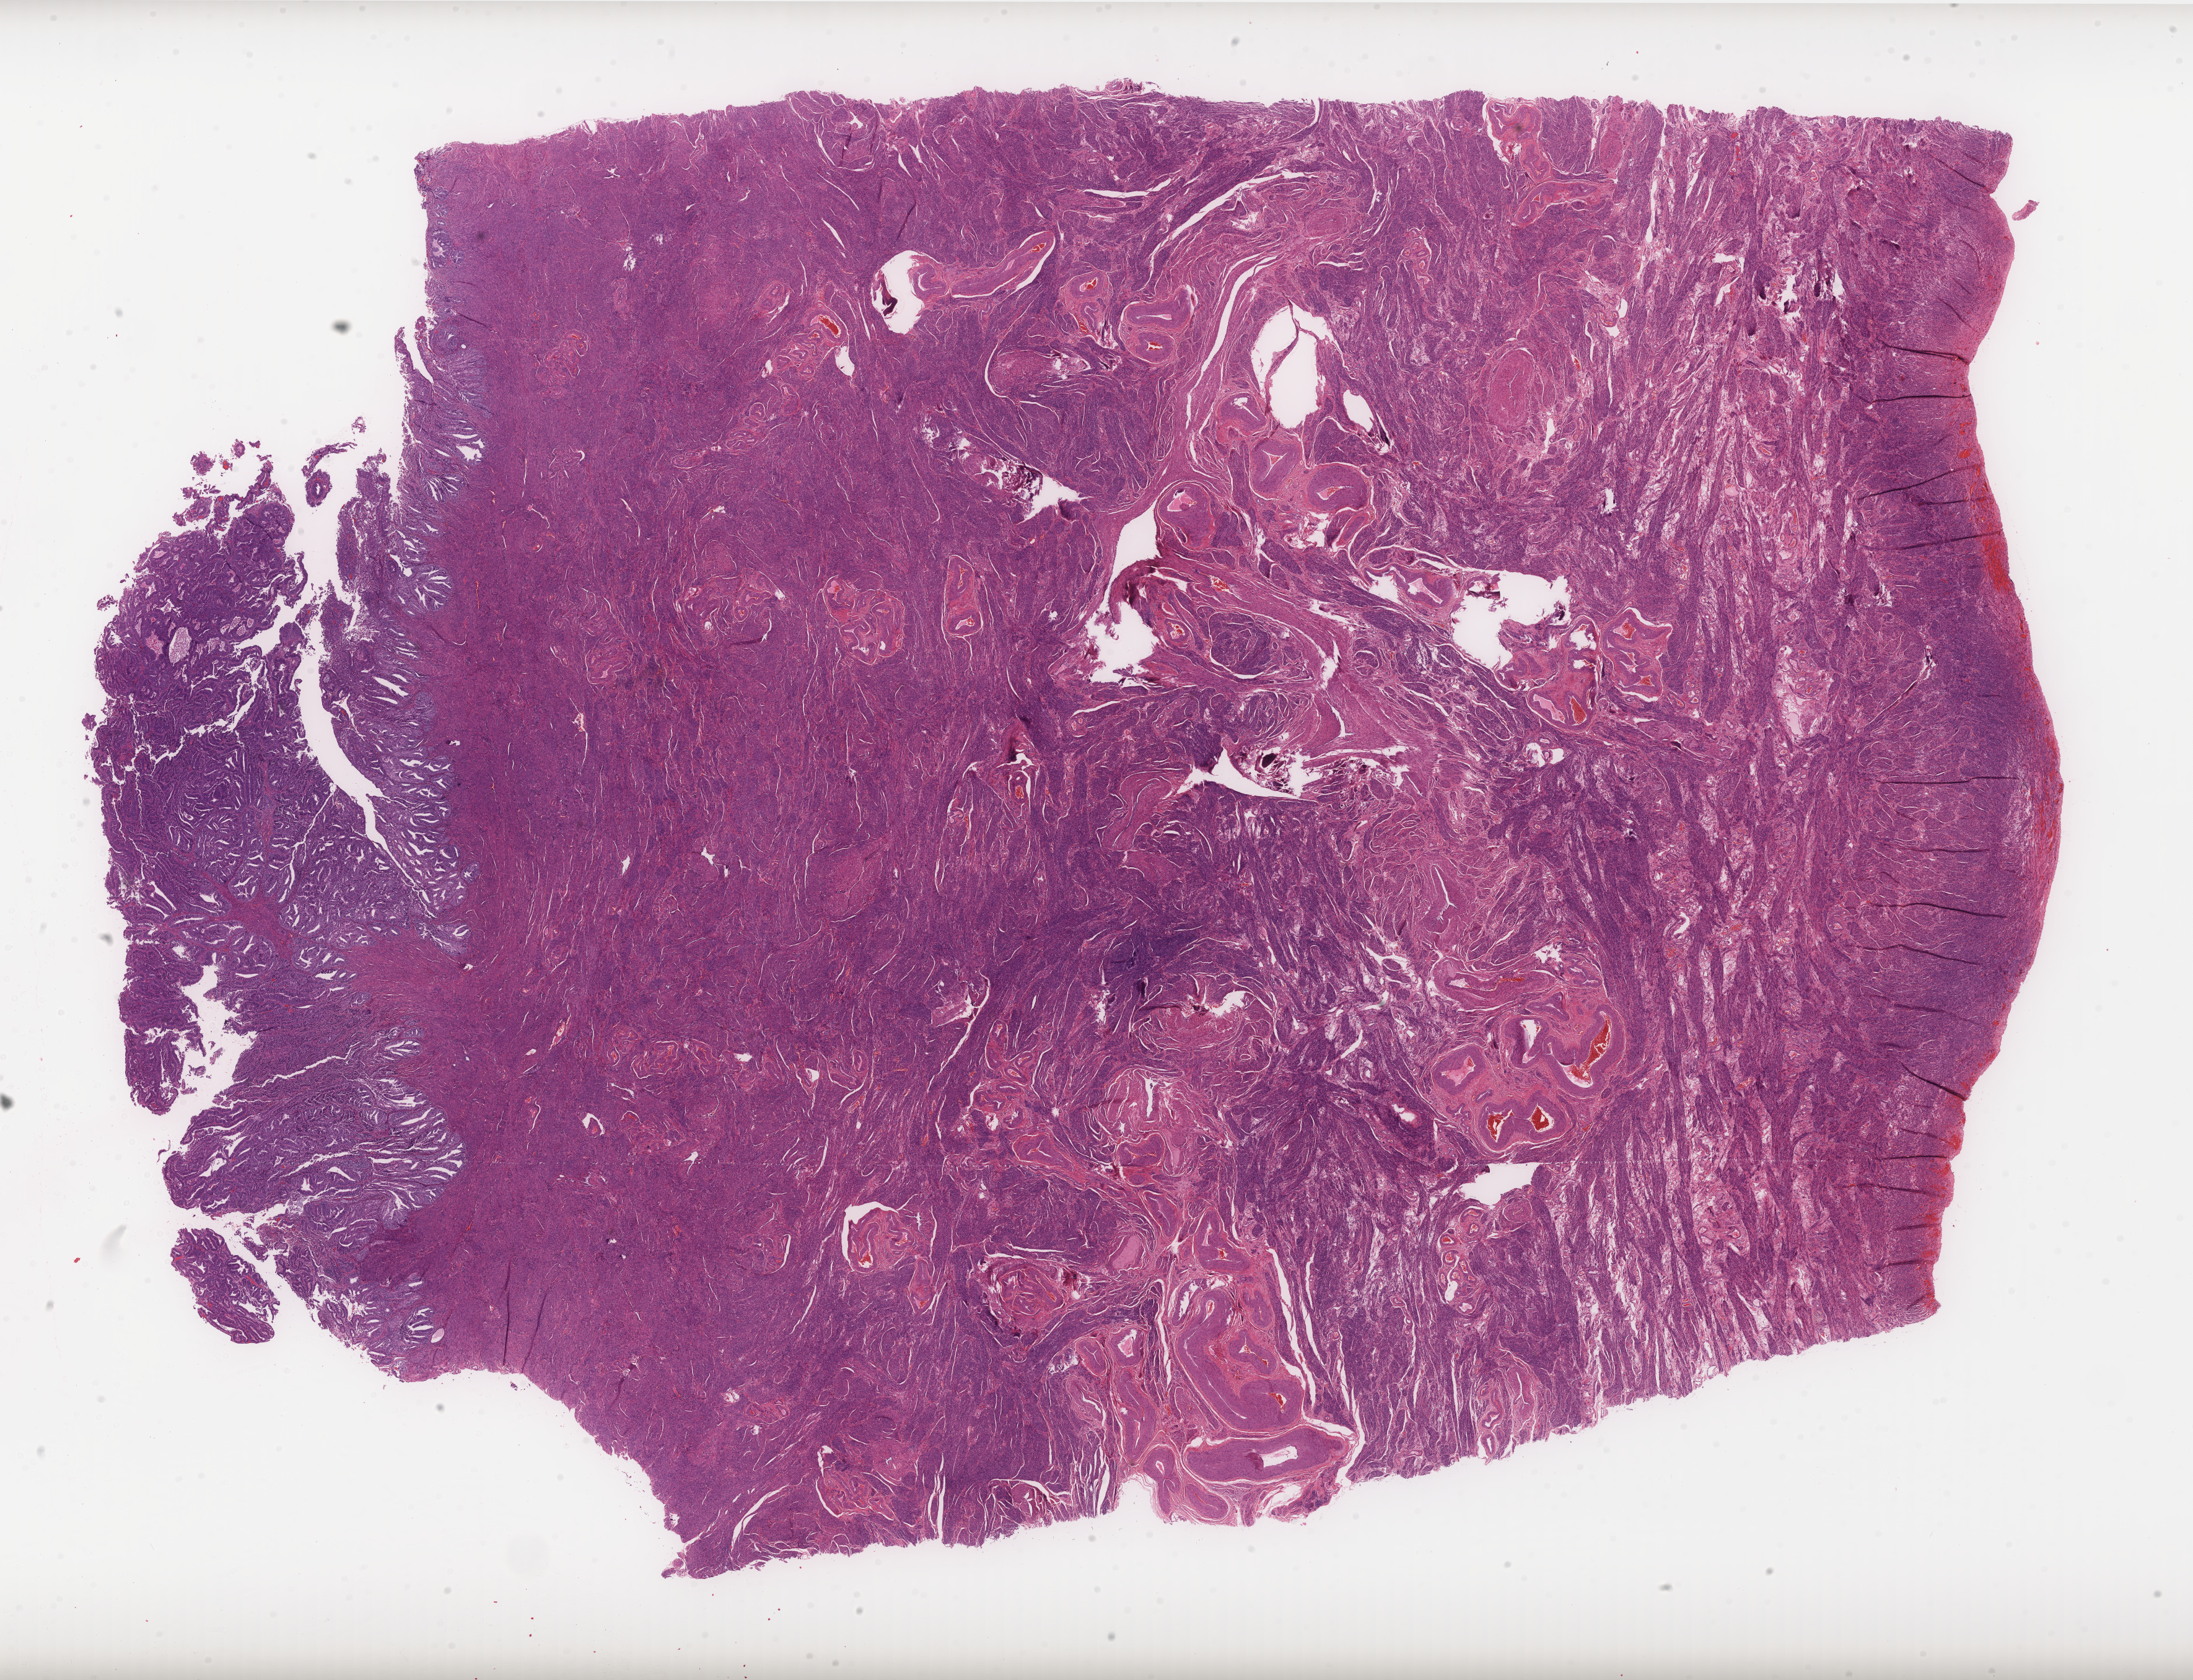
Hematoxylin and eosin (H&E) stained whole-slide image, whole scanned area (about 28.4 x 21.7 mm, acquisition: 40x scan) shown as a low-resolution overview. Formalin-fixed paraffin-embedded (FFPE) diagnostic section. Sample: primary tumour, uterus. Patient: female, age at initial diagnosis 58 years. Histologic grade: G1 (well differentiated).
* FIGO stage: IA
* diagnosis: Endometrioid adenocarcinoma, NOS (endometrium)